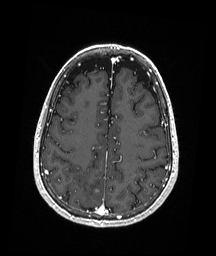
Brain MRI from a brain-tumour surgery series, one axial slice; position 71 of 192 along the scan axis; T1-weighted post-contrast; 1 mm slice thickness; 216 × 256 image matrix, field of view 211 × 250 mm. From the clinical record (not read from this slice): histopathology: Astrocytoma; WHO grade: 3.
Annotated regions visible in this slice (expert manual segmentation):
- tumour: bounding box <89,180,99,192> (left, top, right, bottom; pixels)